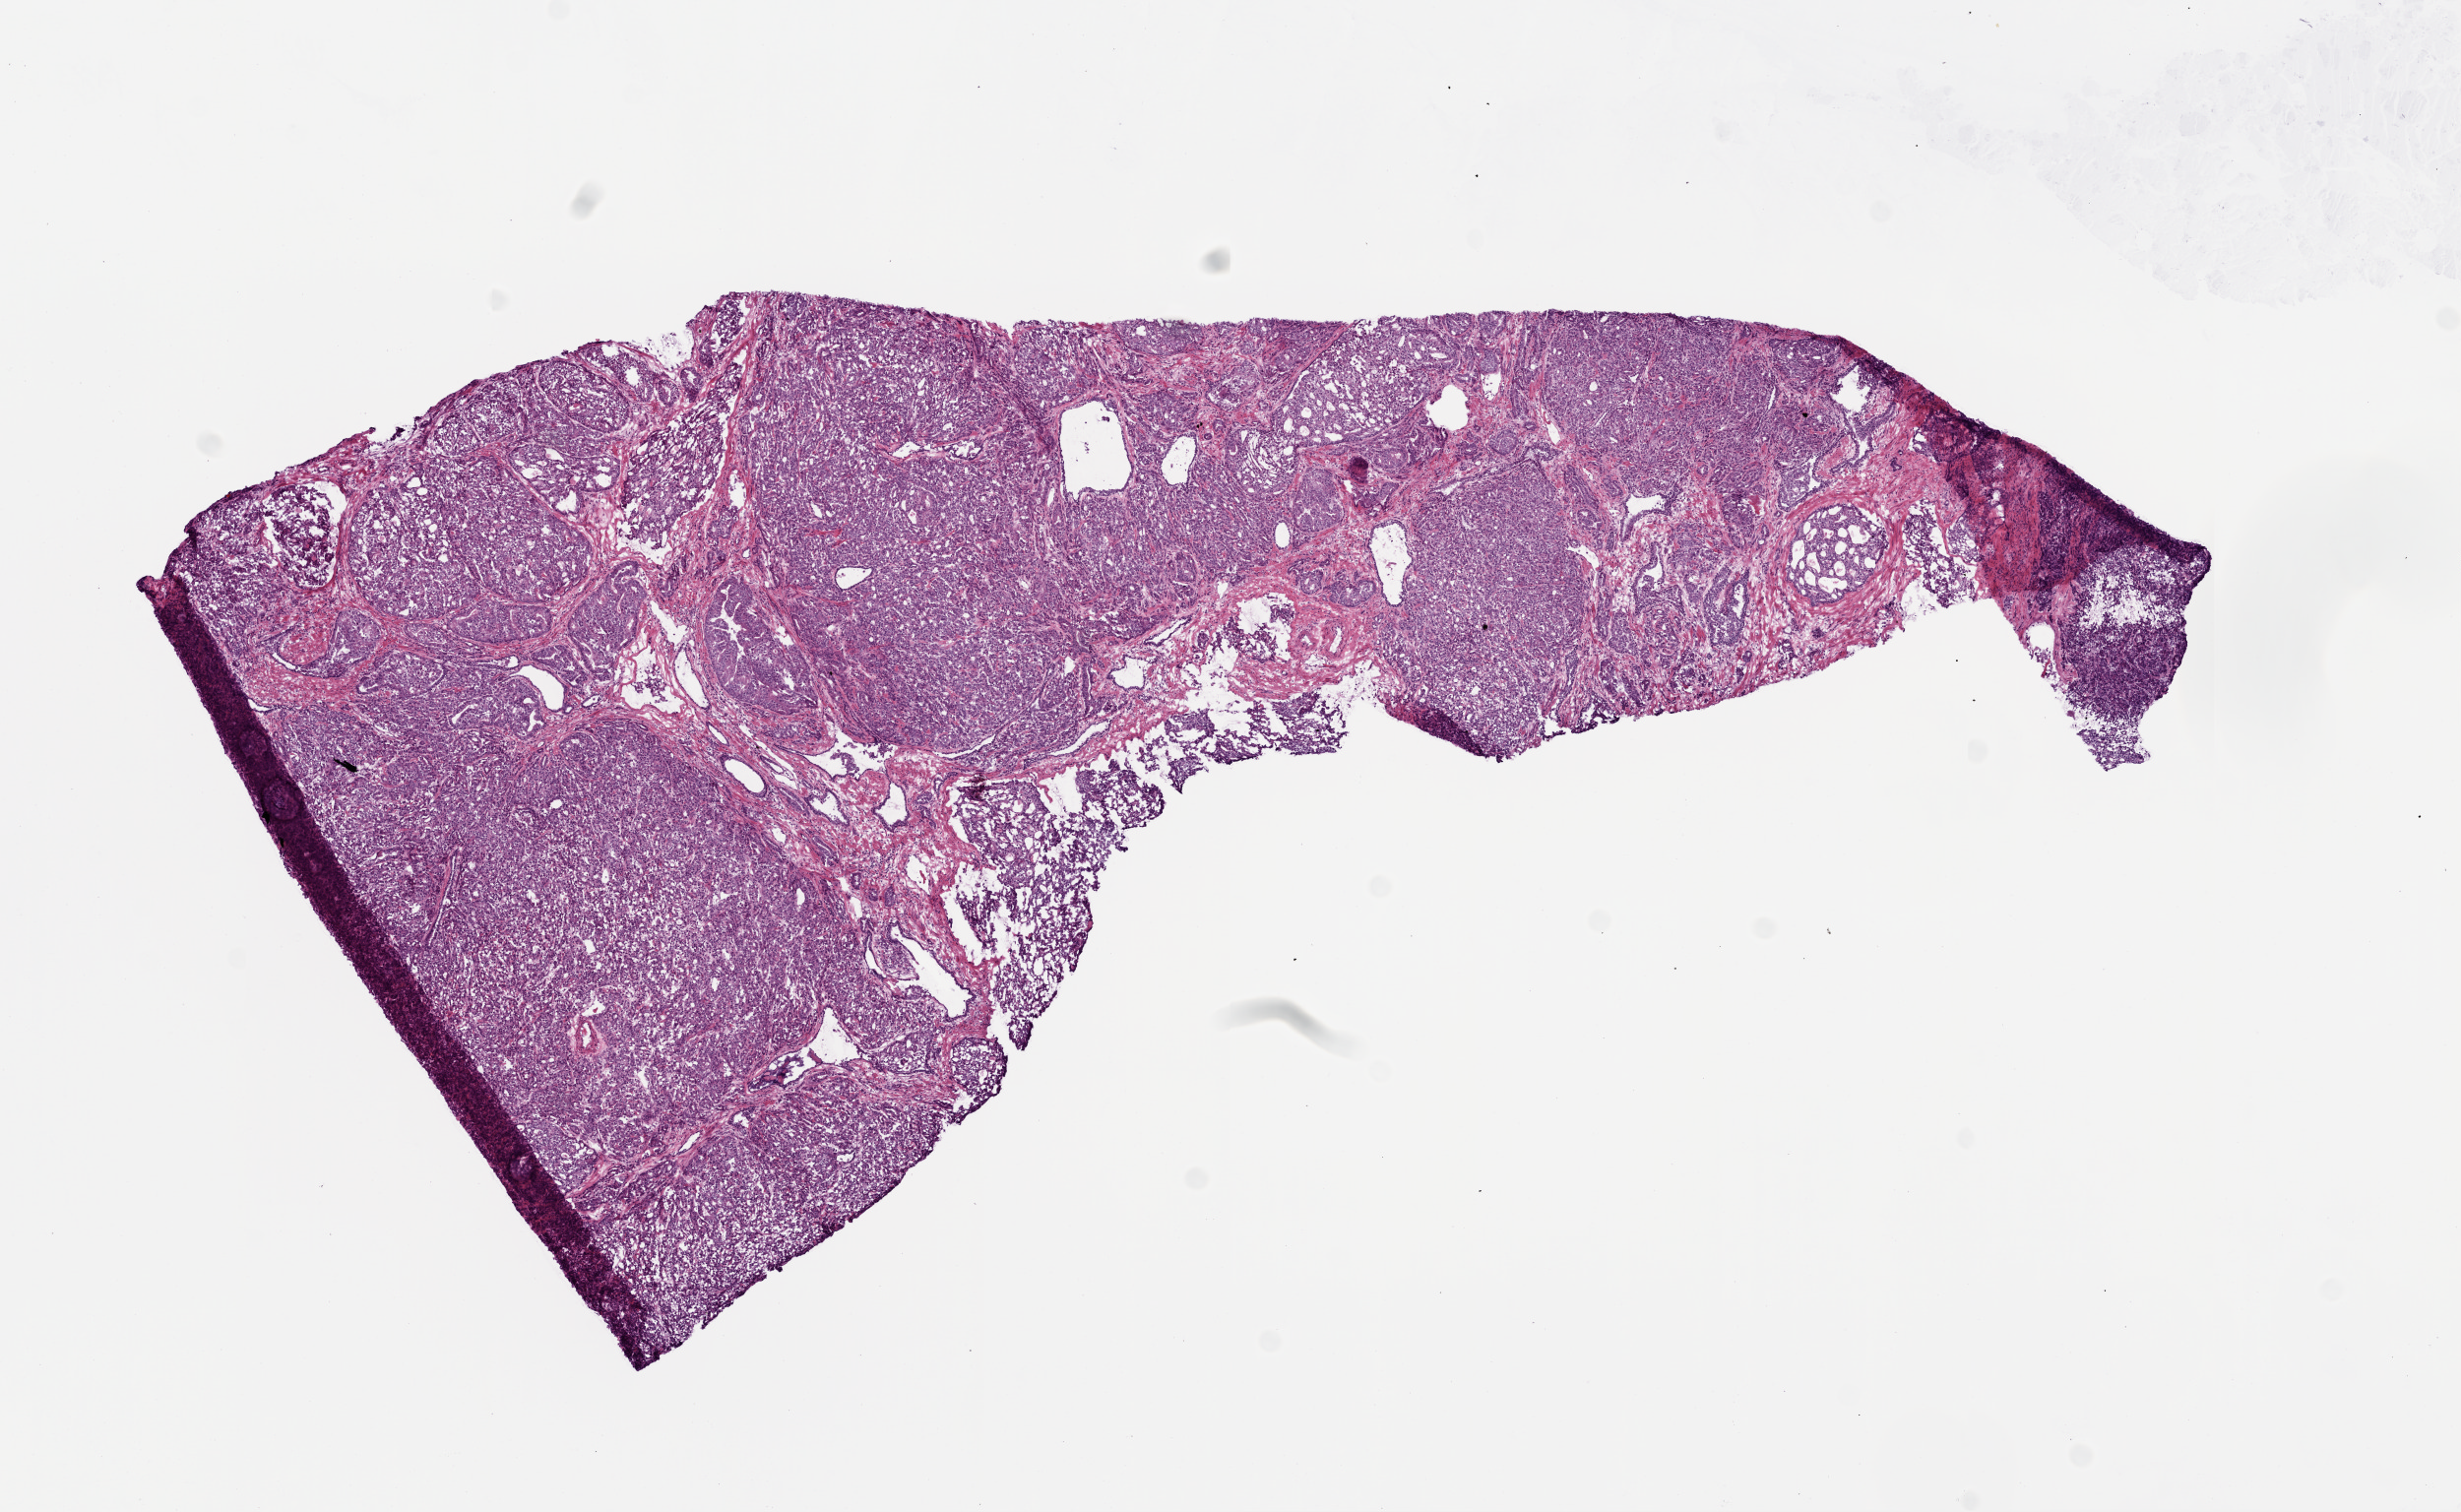
Whole-slide histology image, H&E-stained, whole scanned area (about 10.0 x 6.2 mm, from a 20x scan) shown as a low-resolution overview, frozen section, sample: primary tumour, prostate. Patient: male, age at initial diagnosis 56 years. Gleason score: 9 (4+5). Pathologist review of this section (percent, as recorded): tumour cells 85%, tumour nuclei 85%, normal cells 5%, stromal cells 10%, necrosis 0%. Infiltration values recorded for this section: lymphocyte infiltration 0%, monocyte infiltration 0%, neutrophil infiltration 0%.
Diagnosis: Acinar cell carcinoma (prostate gland). Lymph nodes positive (case pathology): 1 of 5 examined.